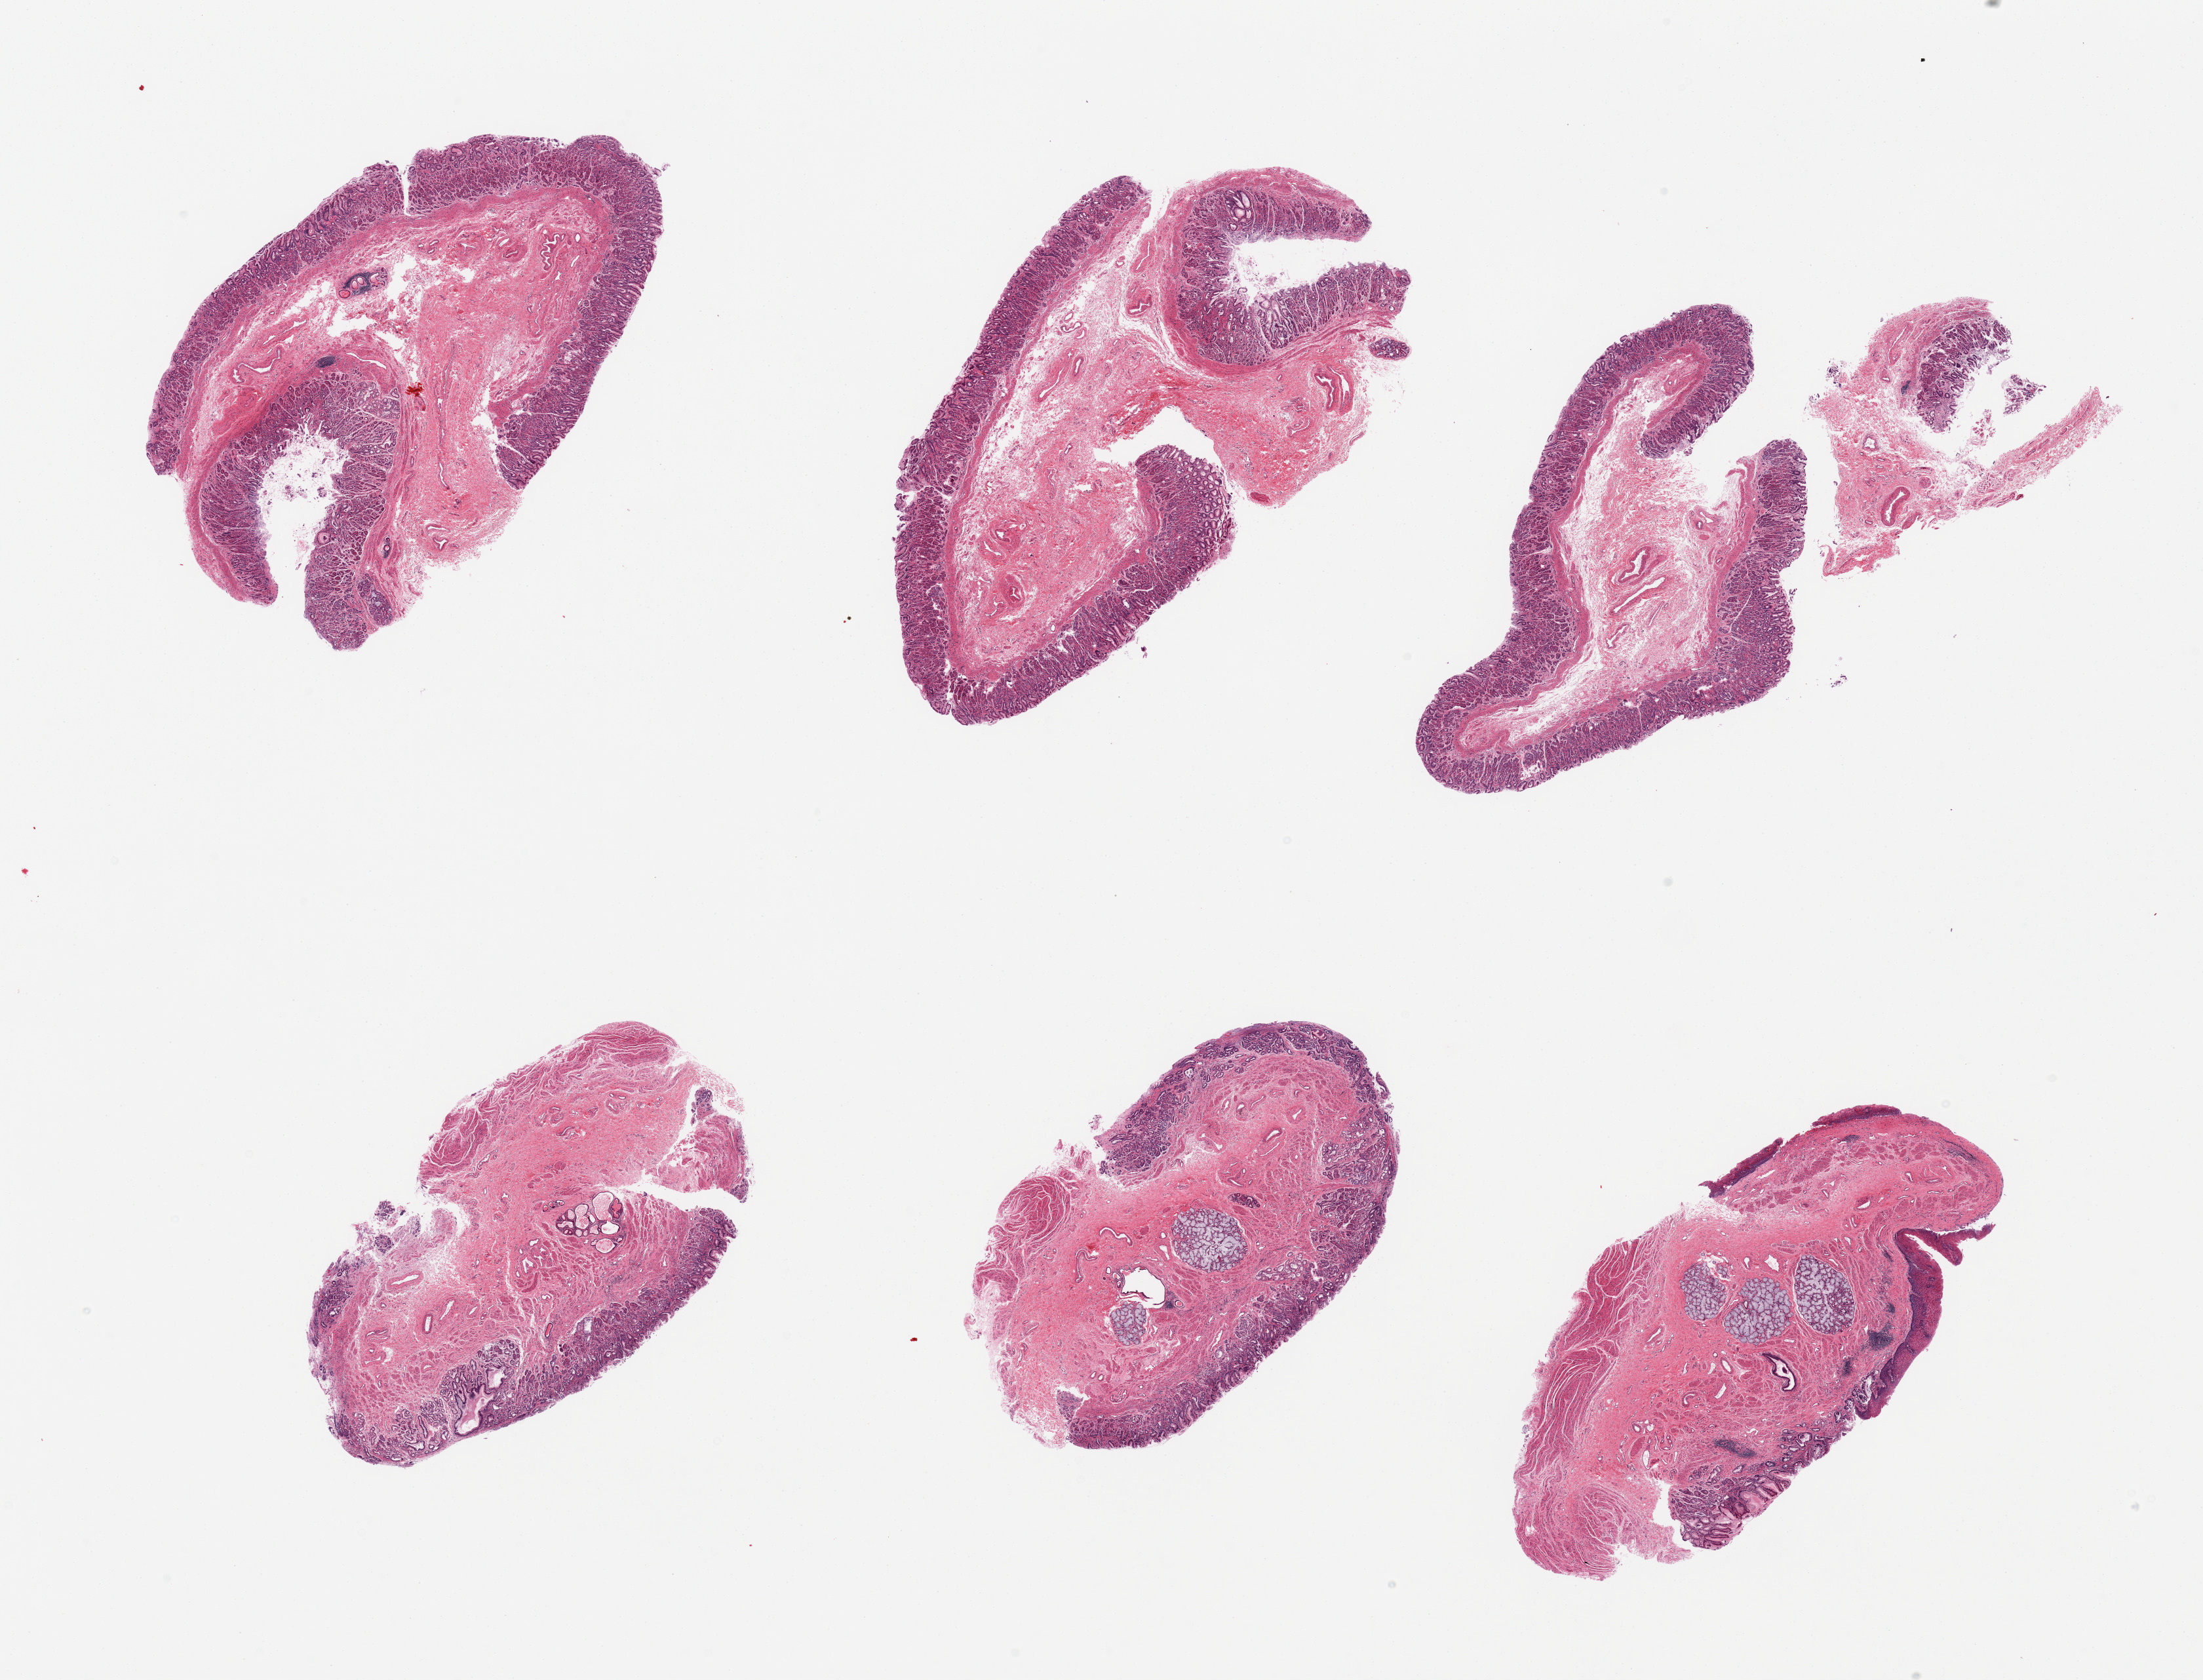
Digitized H&E-stained section, brightfield, low-resolution overview of the scanned area, about 26.6 x 20.3 mm (acquisition: 20x scan); PAXgene-fixed paraffin-embedded (PFPE) section; section of gastroesophageal junction (target tissue); donor tissue sample. Donor sex: male.
* review note (as recorded): 6 pieces, all with esophagogastric mucosa, little muscle